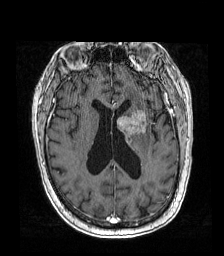
Brain MRI from a brain-tumour surgery series, one axial slice. Position 74 of 192 along the scan axis. T1-weighted post-contrast. 1 mm slice thickness. 224 × 256 image matrix. From the clinical record (not read from this slice): histopathology: Metastatic carcinoma from lung primary.
Structures marked on this image (expert manual segmentation):
- tumour: bounding box <117,110,148,145> (left, top, right, bottom; pixels)